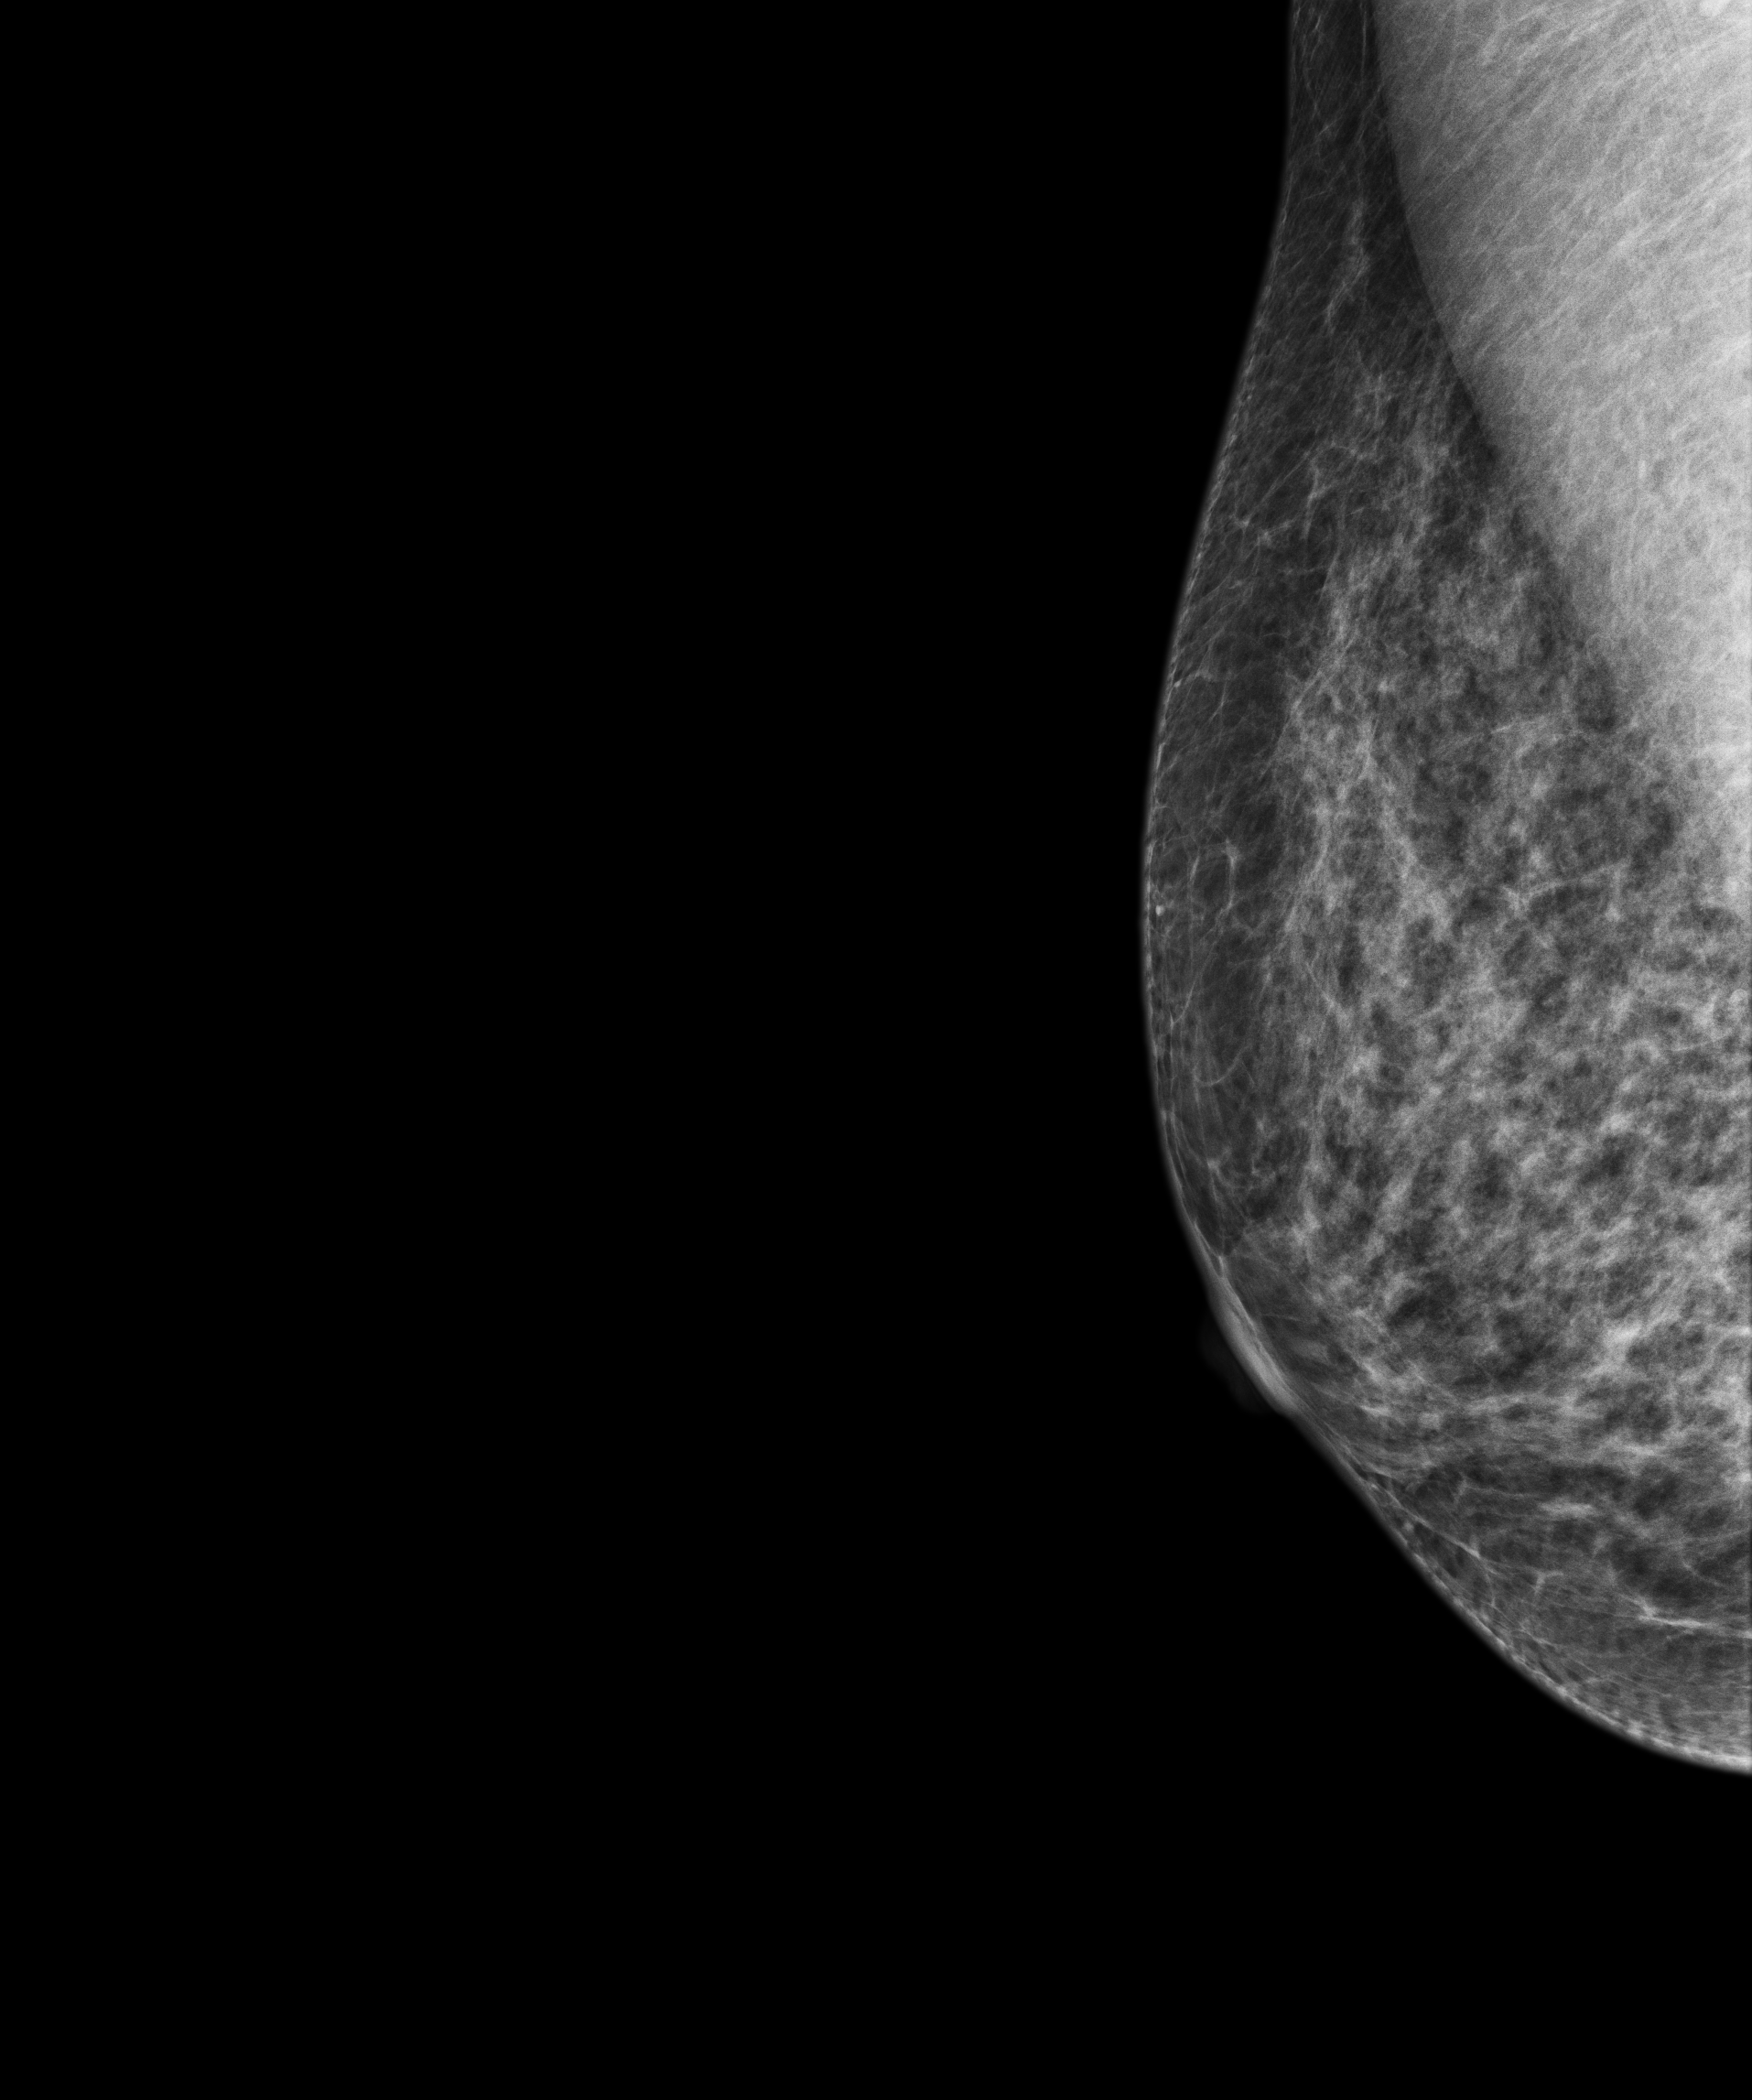
Screening examination, compressed breast thickness 54 mm. Female patient, age 70 years.
Image type: full-field digital mammogram. Breast: right. Projection: laterally exaggerated craniocaudal (XCCL) view.